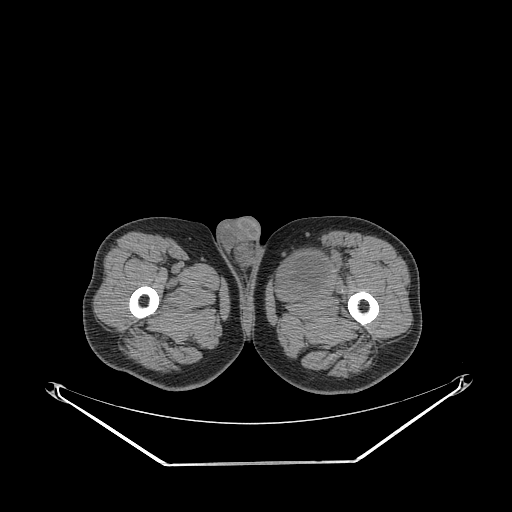
CT of an extremity soft-tissue mass (from a PET/CT study), one axial slice. Slice 262 of 267 in the series (ordered by position). 140 kVp. Soft-tissue window (W 400 / L 40 HU). 3.75 mm slice thickness. 512 × 512 image matrix. Male patient. Case-level facts recorded for this patient, not image findings: histological type: pleiomorphic liposarcoma; grade: high; site of the primary tumour: left thigh.
Structures marked on this image (expert contour drawn on MRI and transferred to this co-registered scan by the dataset authors):
- gross tumour volume including surrounding oedema: bounding box <281,242,346,295> (left, top, right, bottom; pixels)
- gross tumour volume (mass): <281,251,328,289>